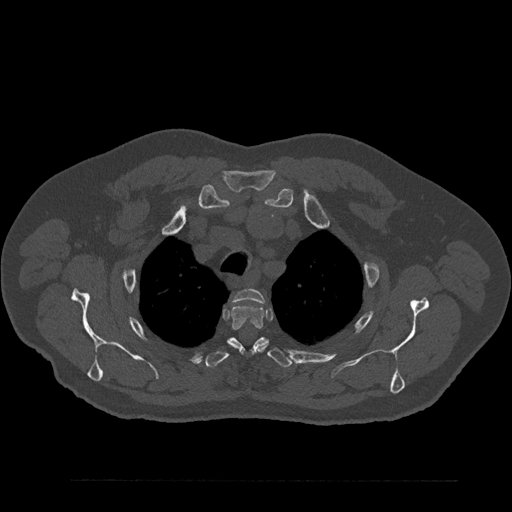
CT including the spine, one axial slice; position 673 of 797 along the scan axis; reconstruction kernel Br40s/3; 120 kVp; bone window (W 1800 / L 400 HU); 512 × 512 image matrix. Patient: male, 61 years. Case-level facts recorded for this patient, not image findings: primary cancer: prostate.
Annotated regions visible in this slice (semi-automatic segmentation, software-assisted and operator-edited):
- T2 vertebra: bounding box [x1, y1, x2, y2] px = [234, 289, 265, 303]
- T3 vertebra: [231, 304, 266, 352]
- T4 vertebra: [204, 337, 292, 368]